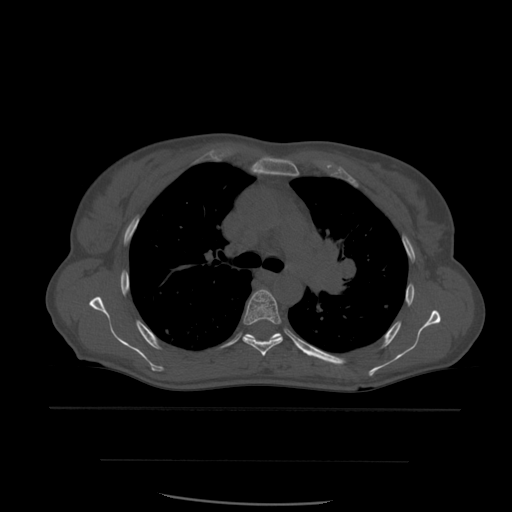
CT including the spine, one axial slice. Slice 407 of 574 in the series (ordered by position). Bone window (W 1800 / L 400 HU). 1.25 mm slice thickness. 512 × 512 image matrix, field of view 392 × 392 mm. Patient age 48 years. Case-level facts recorded for this patient, not image findings: primary cancer: lung; vertebrae with lytic lesions (as recorded): T11.
Structures marked on this image (semi-automatically segmented with operator editing):
- T5 vertebra: box from (x=243, y=290) to (x=283, y=357) px
- T6 vertebra: (x=243, y=333)–(x=282, y=341)